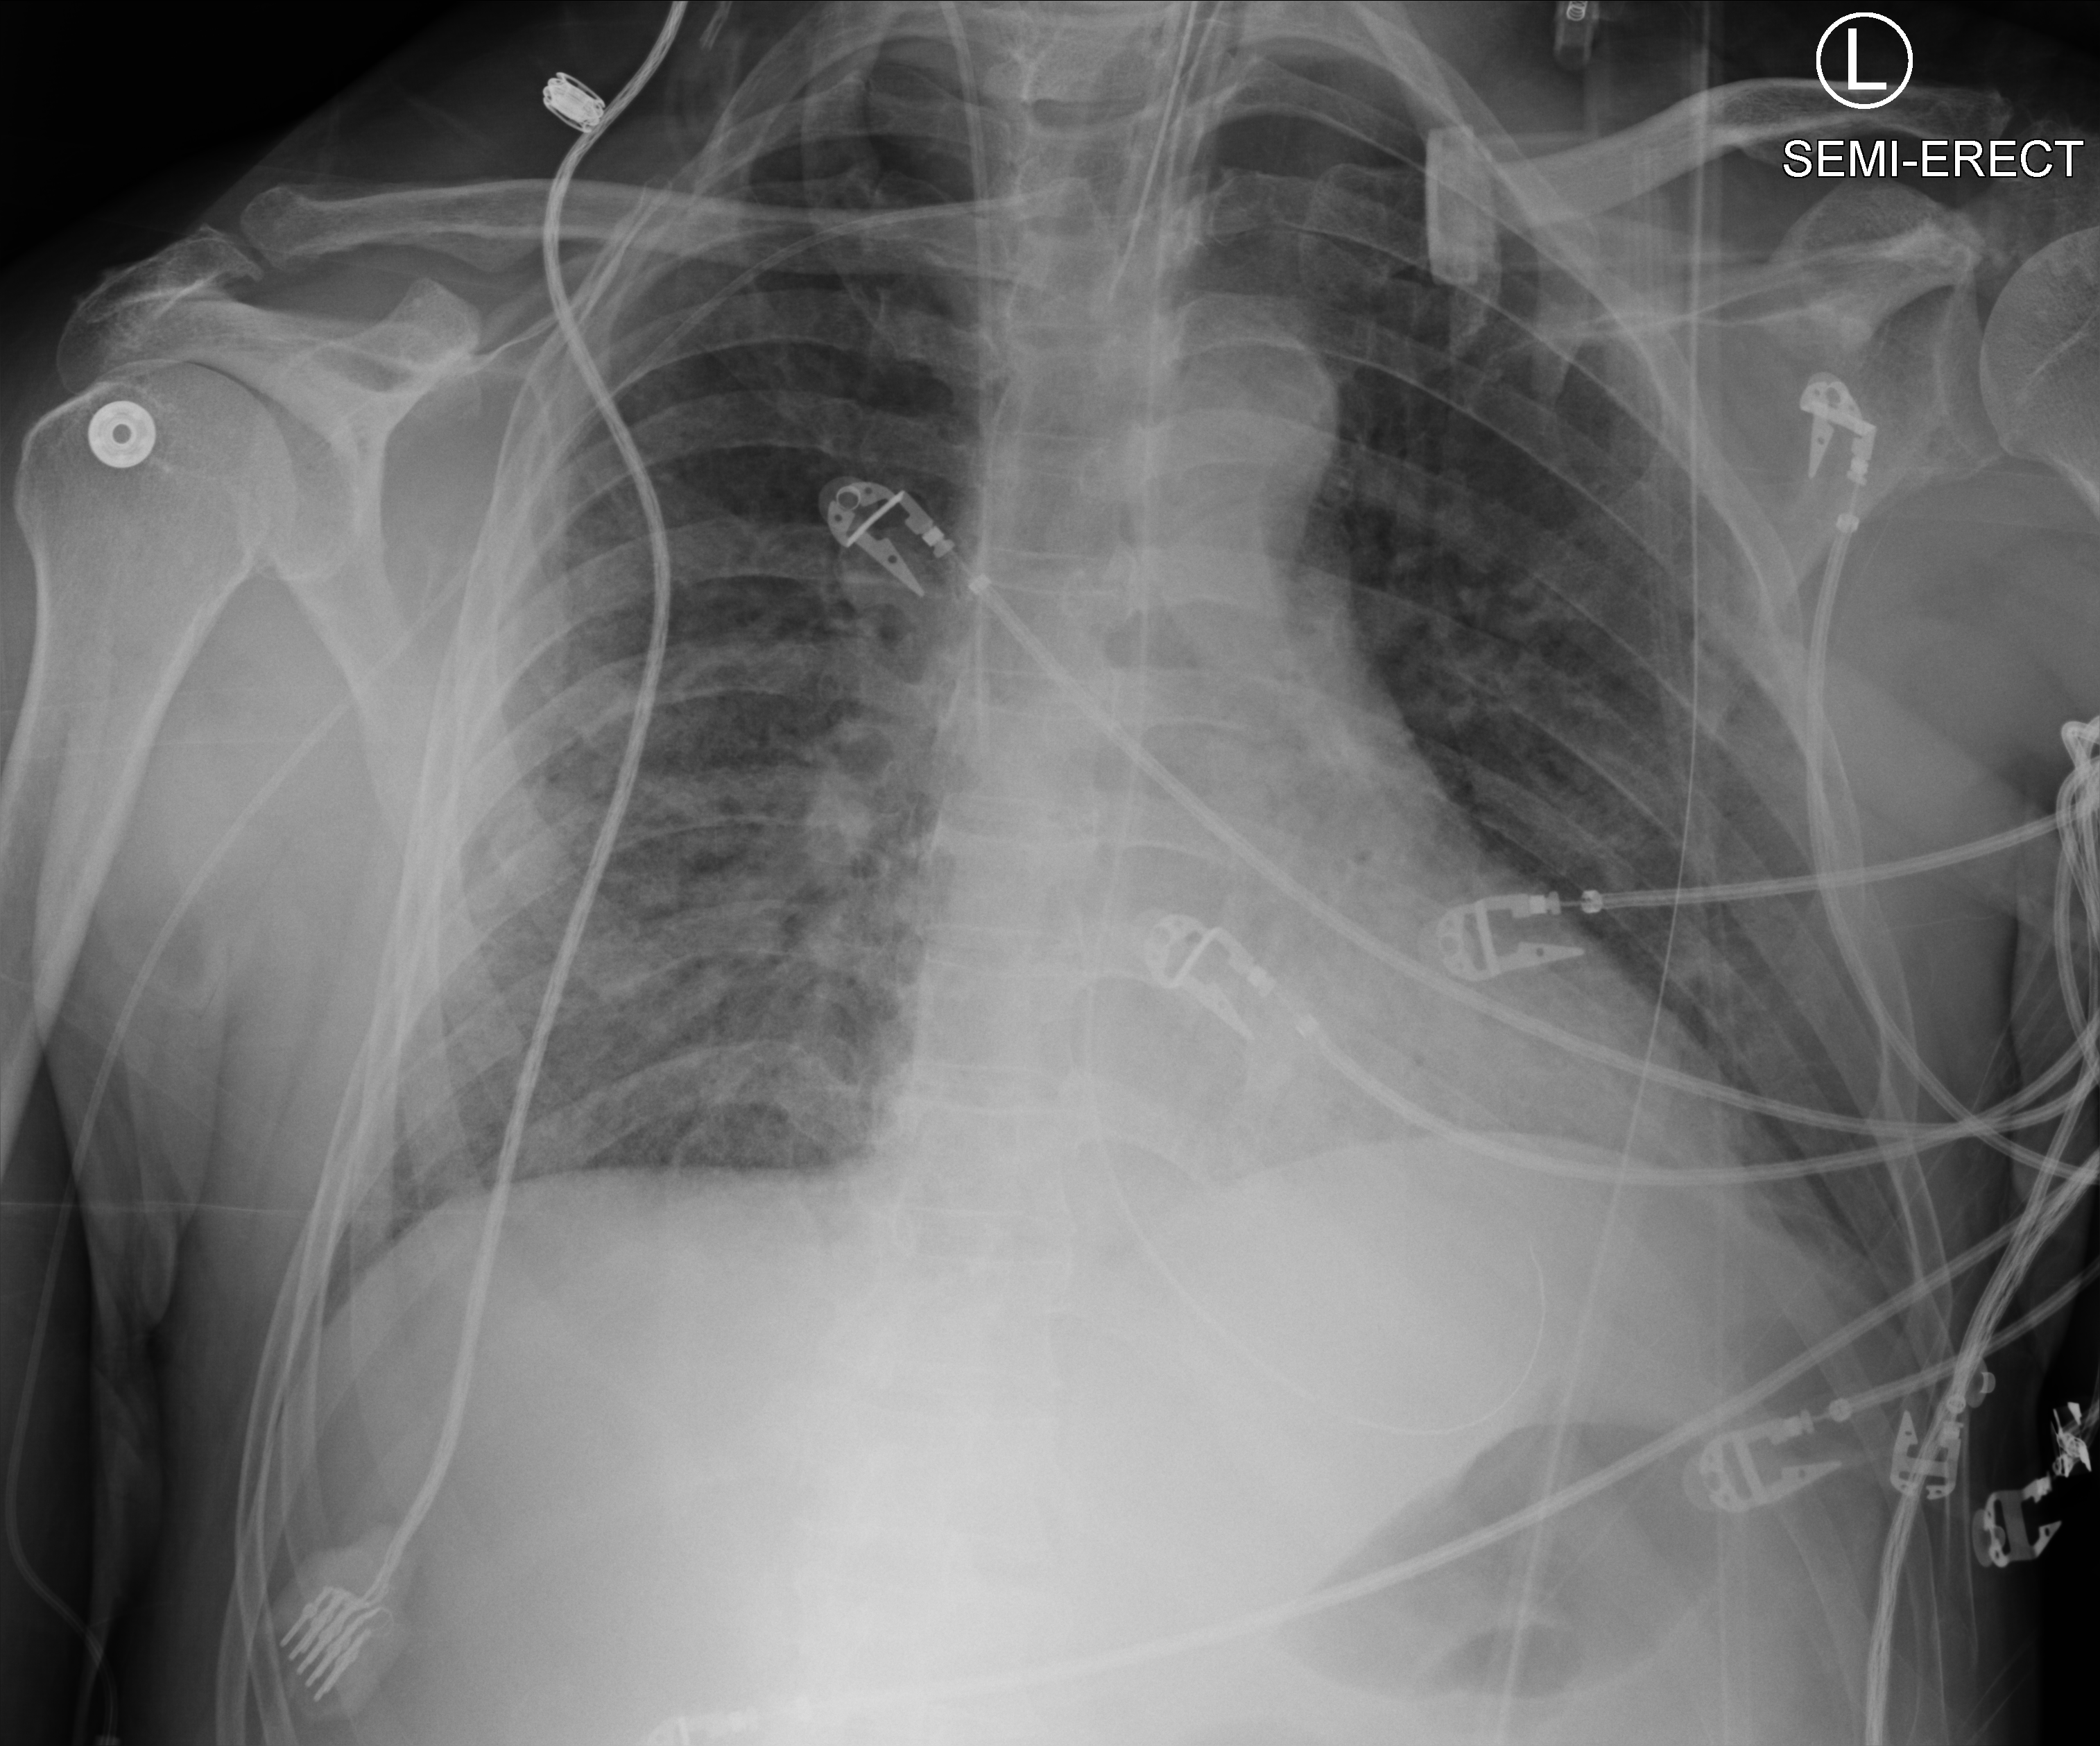
Portable chest radiograph. Patient hospitalised with COVID-19; male, aged 60–74 years.
Hospital-stay facts (about this admission, not read from this image; timing relative to this image not recorded):
- admitted to intensive care during this hospital stay: yes